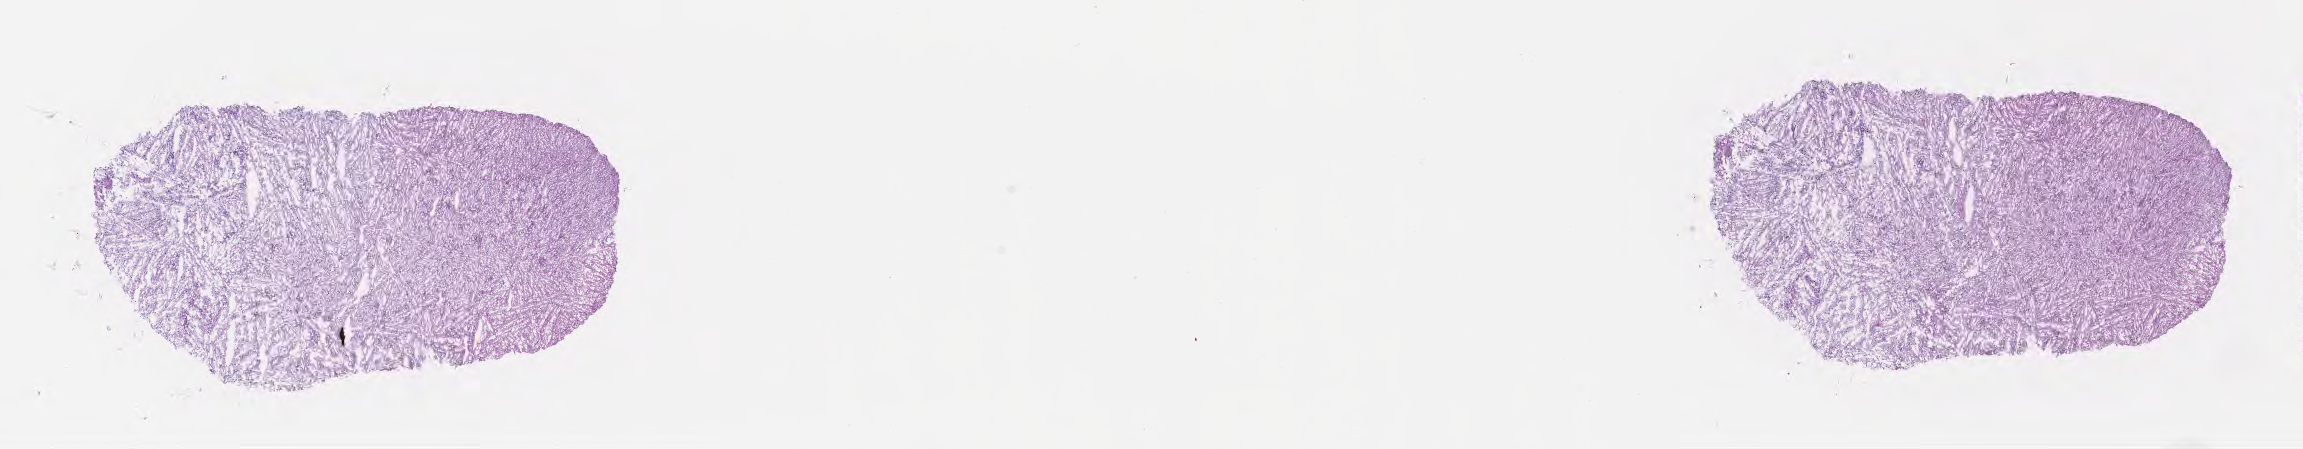
Digitized H&E-stained section — low-resolution overview of the scanned area, about 18.6 x 3.6 mm. Frozen section (tissue freezing medium). Specimen: primary tumor. Site: brain. Male patient; age at initial diagnosis 54 years. Composition of this section per pathologist review: tumor cells 41%, tumor nuclei 72%, stromal cells 43%, necrosis 0%, normal cells 16%. Inflammatory infiltration, as recorded: lymphocyte infiltration 0%, monocyte infiltration 0%, neutrophil infiltration 0%.
* diagnosis: Glioblastoma, NOS